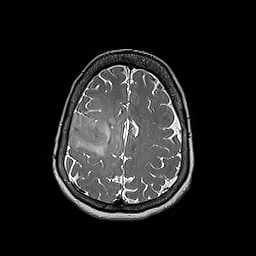
Brain MRI from a brain-tumour surgery series, one axial slice. Position 63 of 192 along the scan axis. 1 mm slice thickness. 256 × 256 image matrix, field of view 250 × 250 mm. Case-level facts recorded for this patient, not image findings: histopathology: Oligodendroglioma; WHO grade: 3; IDH mutation: yes.
Annotated regions visible in this slice (manually delineated by an expert):
- tumour: box from (x=68, y=112) to (x=108, y=148) px